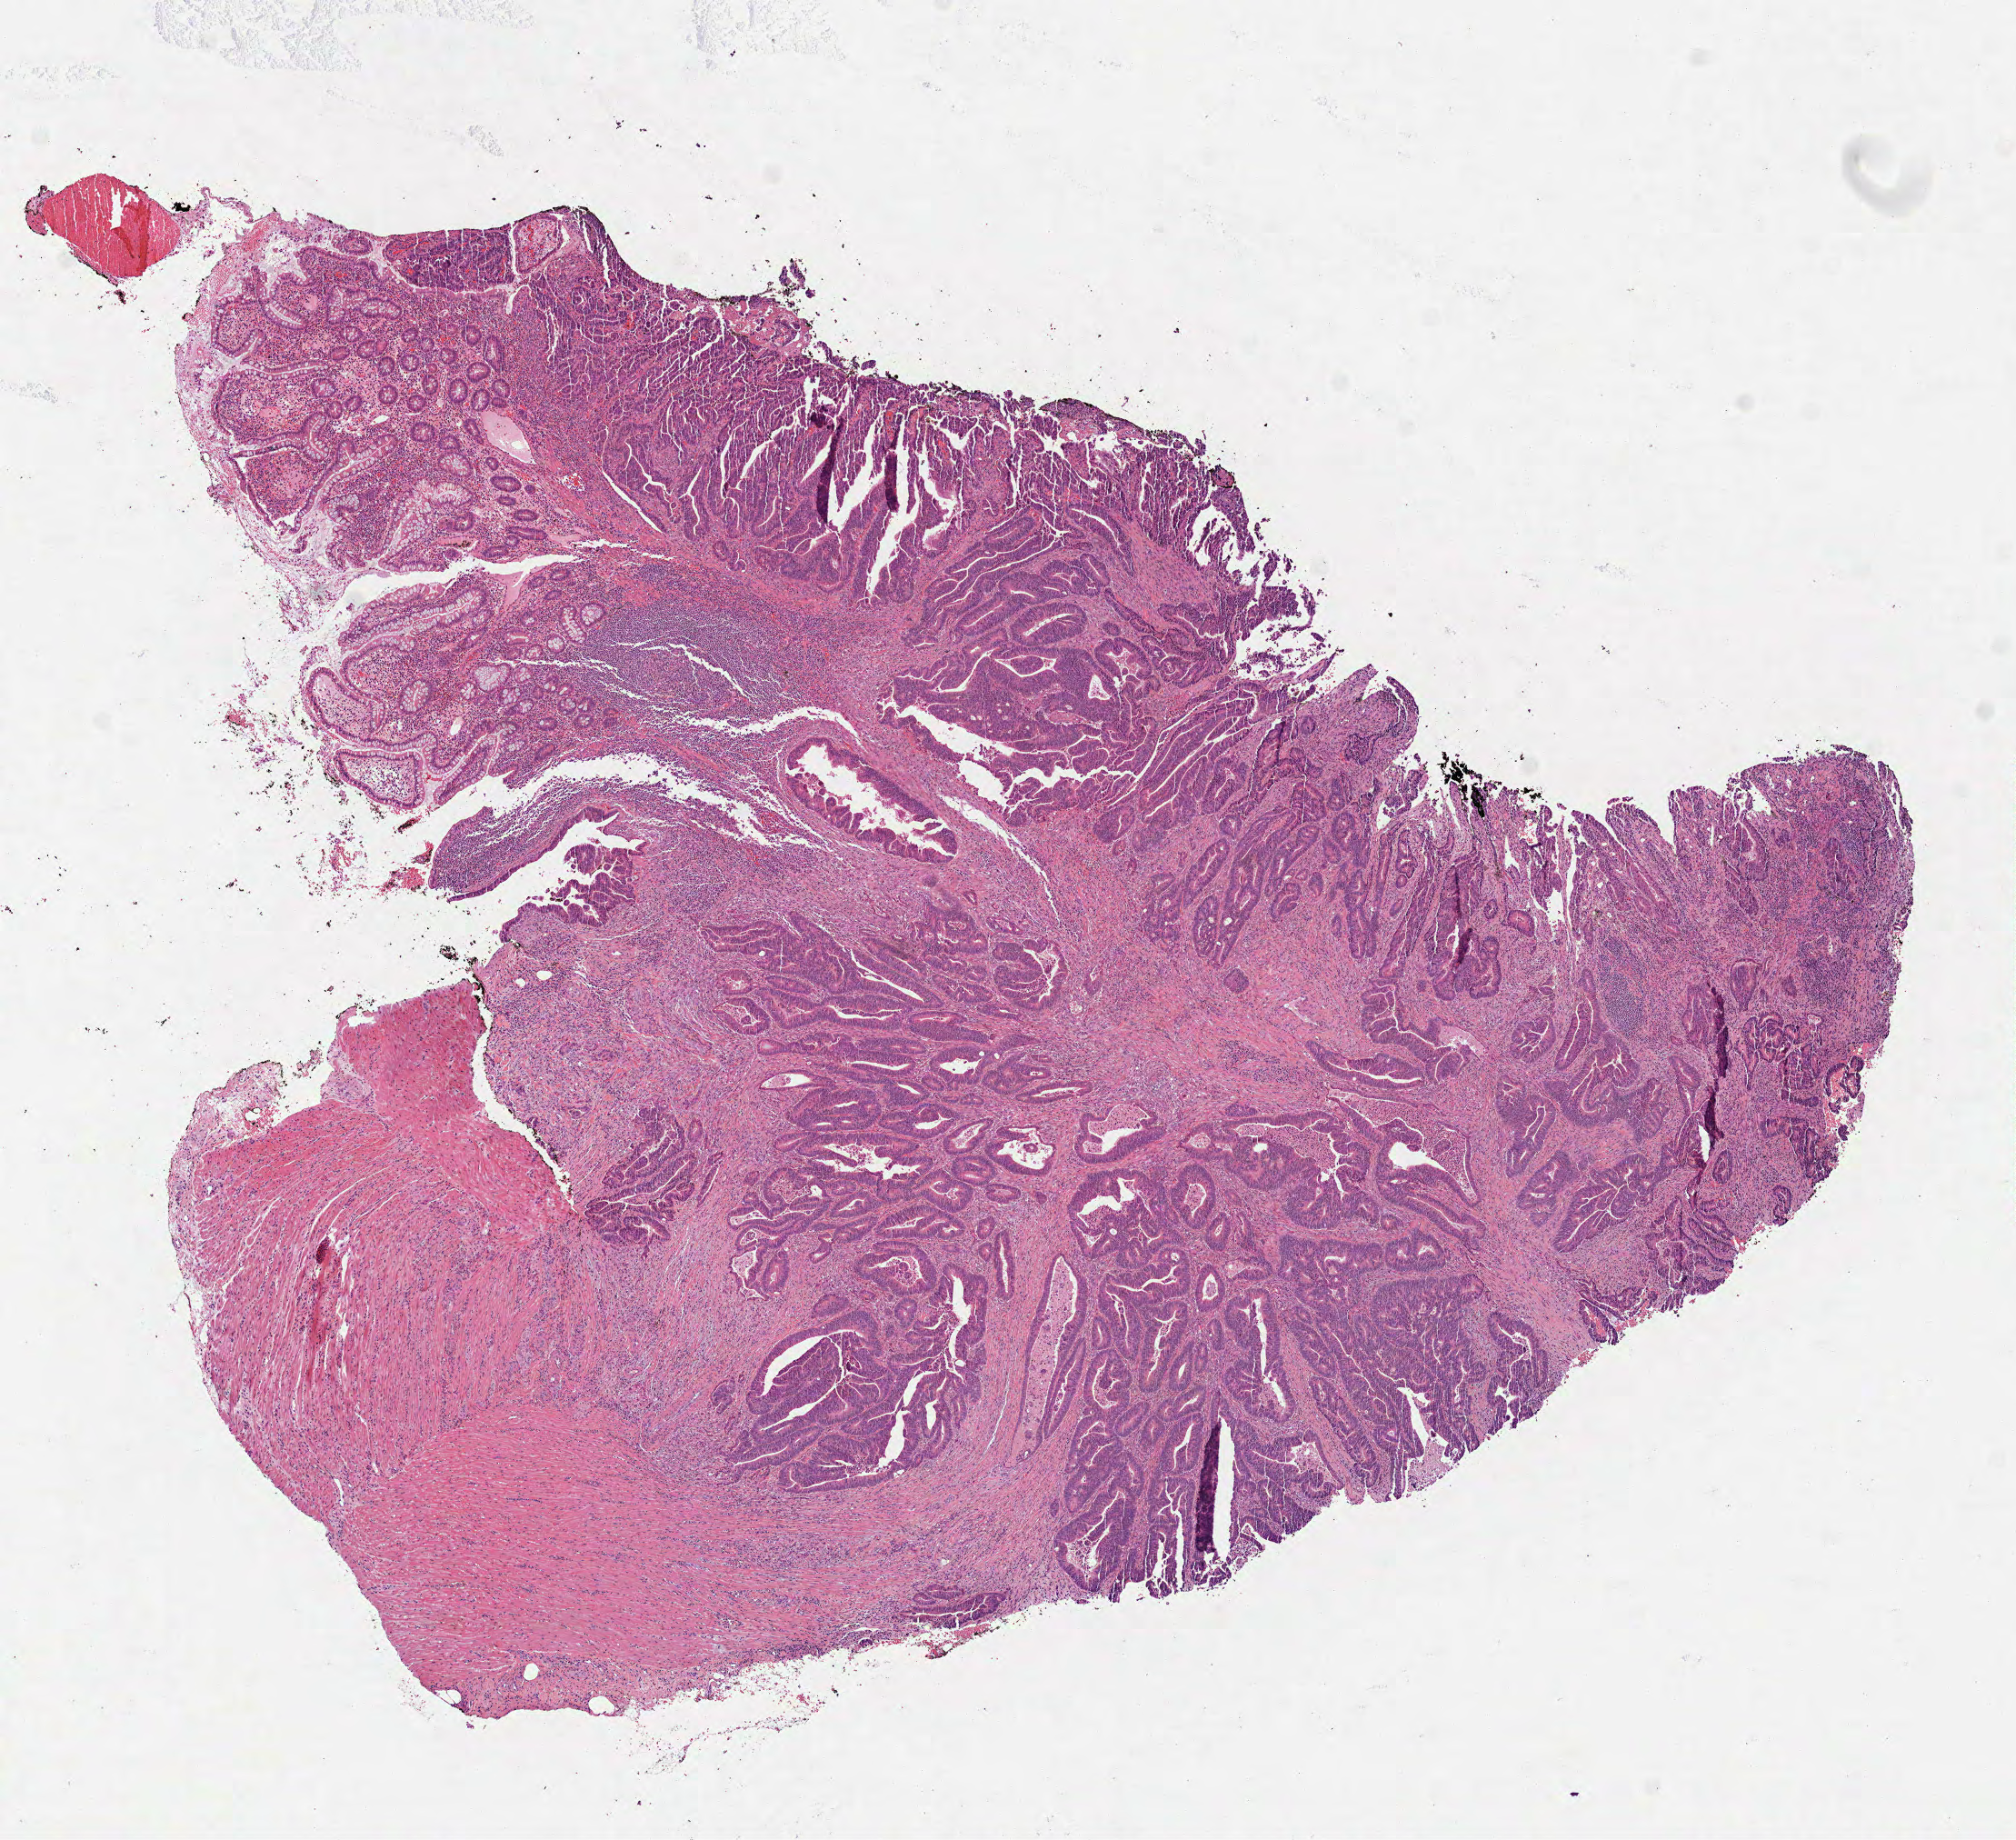
Digitized Hematoxylin and eosin (H&E) stained tissue section (whole slide), shown as a low-resolution overview of the whole scanned area (about 8.9 x 8.2 mm, slide scanned at 40x); FFPE section; primary tumour sample from the colon. Male patient; age at initial diagnosis 78 years.
- lymph nodes positive (case pathology): 0 of 19 examined
- histologic diagnosis: Adenocarcinoma, NOS (cecum)